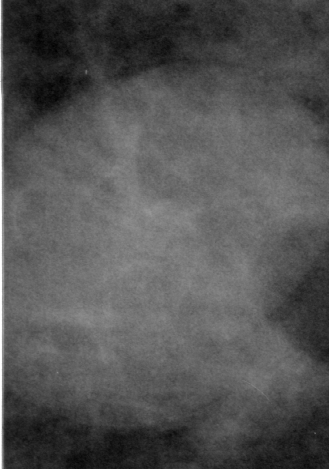
Cropped region of a digitized screen-film mammogram centred on a radiologist-marked abnormality, left breast, CC view, BI-RADS breast density category 2 (scale 1–4).
Mass, shape round / oval, margins circumscribed / obscured; BI-RADS assessment category 4; pathology result (as recorded, not read from the image): benign.